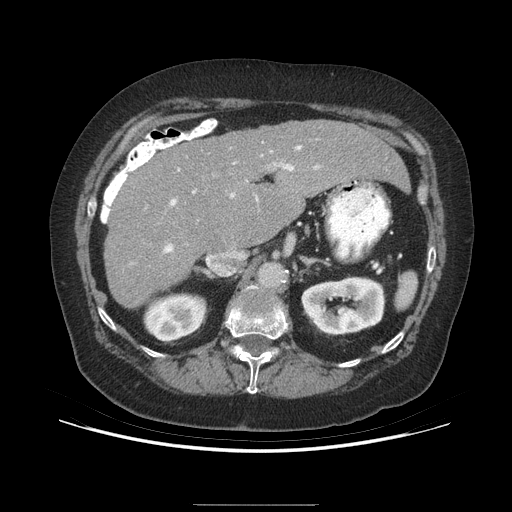
Contrast-enhanced abdominal CT (liver protocol), one axial slice; position 155 of 192 along the scan axis; soft-tissue window (W 400 / L 40 HU); 2.5 mm slice thickness; 512 × 512 image matrix. Case-level facts recorded for this patient, not image findings: diagnosis: hepatocellular carcinoma (patient treated with transarterial chemoembolisation; whether this scan precedes or follows treatment is not stated here); TNM stage (as recorded): Stage-I; Child-Pugh class: A; tumour differentiation: moderately differentiated; tumour nodularity: uninodular.
Structures marked on this image (semi-automatic segmentation, software-assisted and operator-edited):
- liver parenchyma outside the tumour (the mass and vessels are separate outlines, so this box may not span the whole liver): bounding box [x1, y1, x2, y2] px = [104, 120, 408, 308]
- liver vessels: [163, 146, 319, 253]